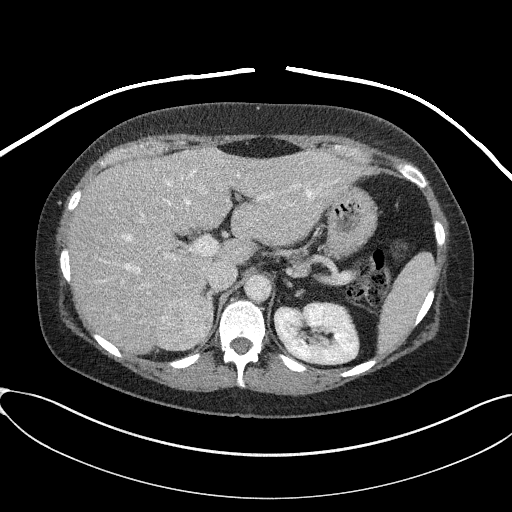
Contrast-enhanced abdominal CT, one axial slice; position 58 of 95 along the scan axis; reconstruction kernel I41f/2; intravenous contrast given; soft-tissue window (W 400 / L 40 HU); 512 × 512 image matrix, field of view 410 × 410 mm. Female patient, age 46 years. From the clinical record (not read from this slice): diagnosis: adrenocortical carcinoma; tumour side: right adrenal; tumour size at pathology: 7.2 cm; Ki-67 index: 50 %; stage (as recorded): 4.
Outlined on this slice (semi-automatically segmented with operator editing):
- mass: bounding box [x1, y1, x2, y2] px = [156, 295, 211, 349]